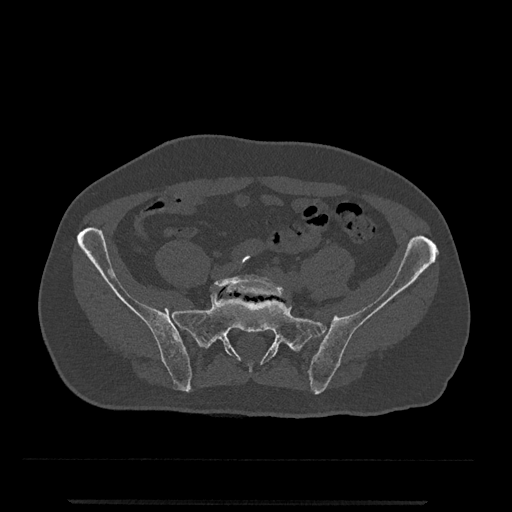
CT including the spine, one axial slice. Position 23 of 797 along the scan axis. Bone window (W 1800 / L 400 HU). 0.5 mm slice thickness. 512 × 512 image matrix, field of view 419 × 419 mm. Male patient, age 63 years. Case-level facts recorded for this patient, not image findings: primary cancer: prostate.
Outlined on this slice (semi-automatic segmentation, software-assisted and operator-edited):
- L5 vertebra: box from (x=210, y=275) to (x=285, y=298) px